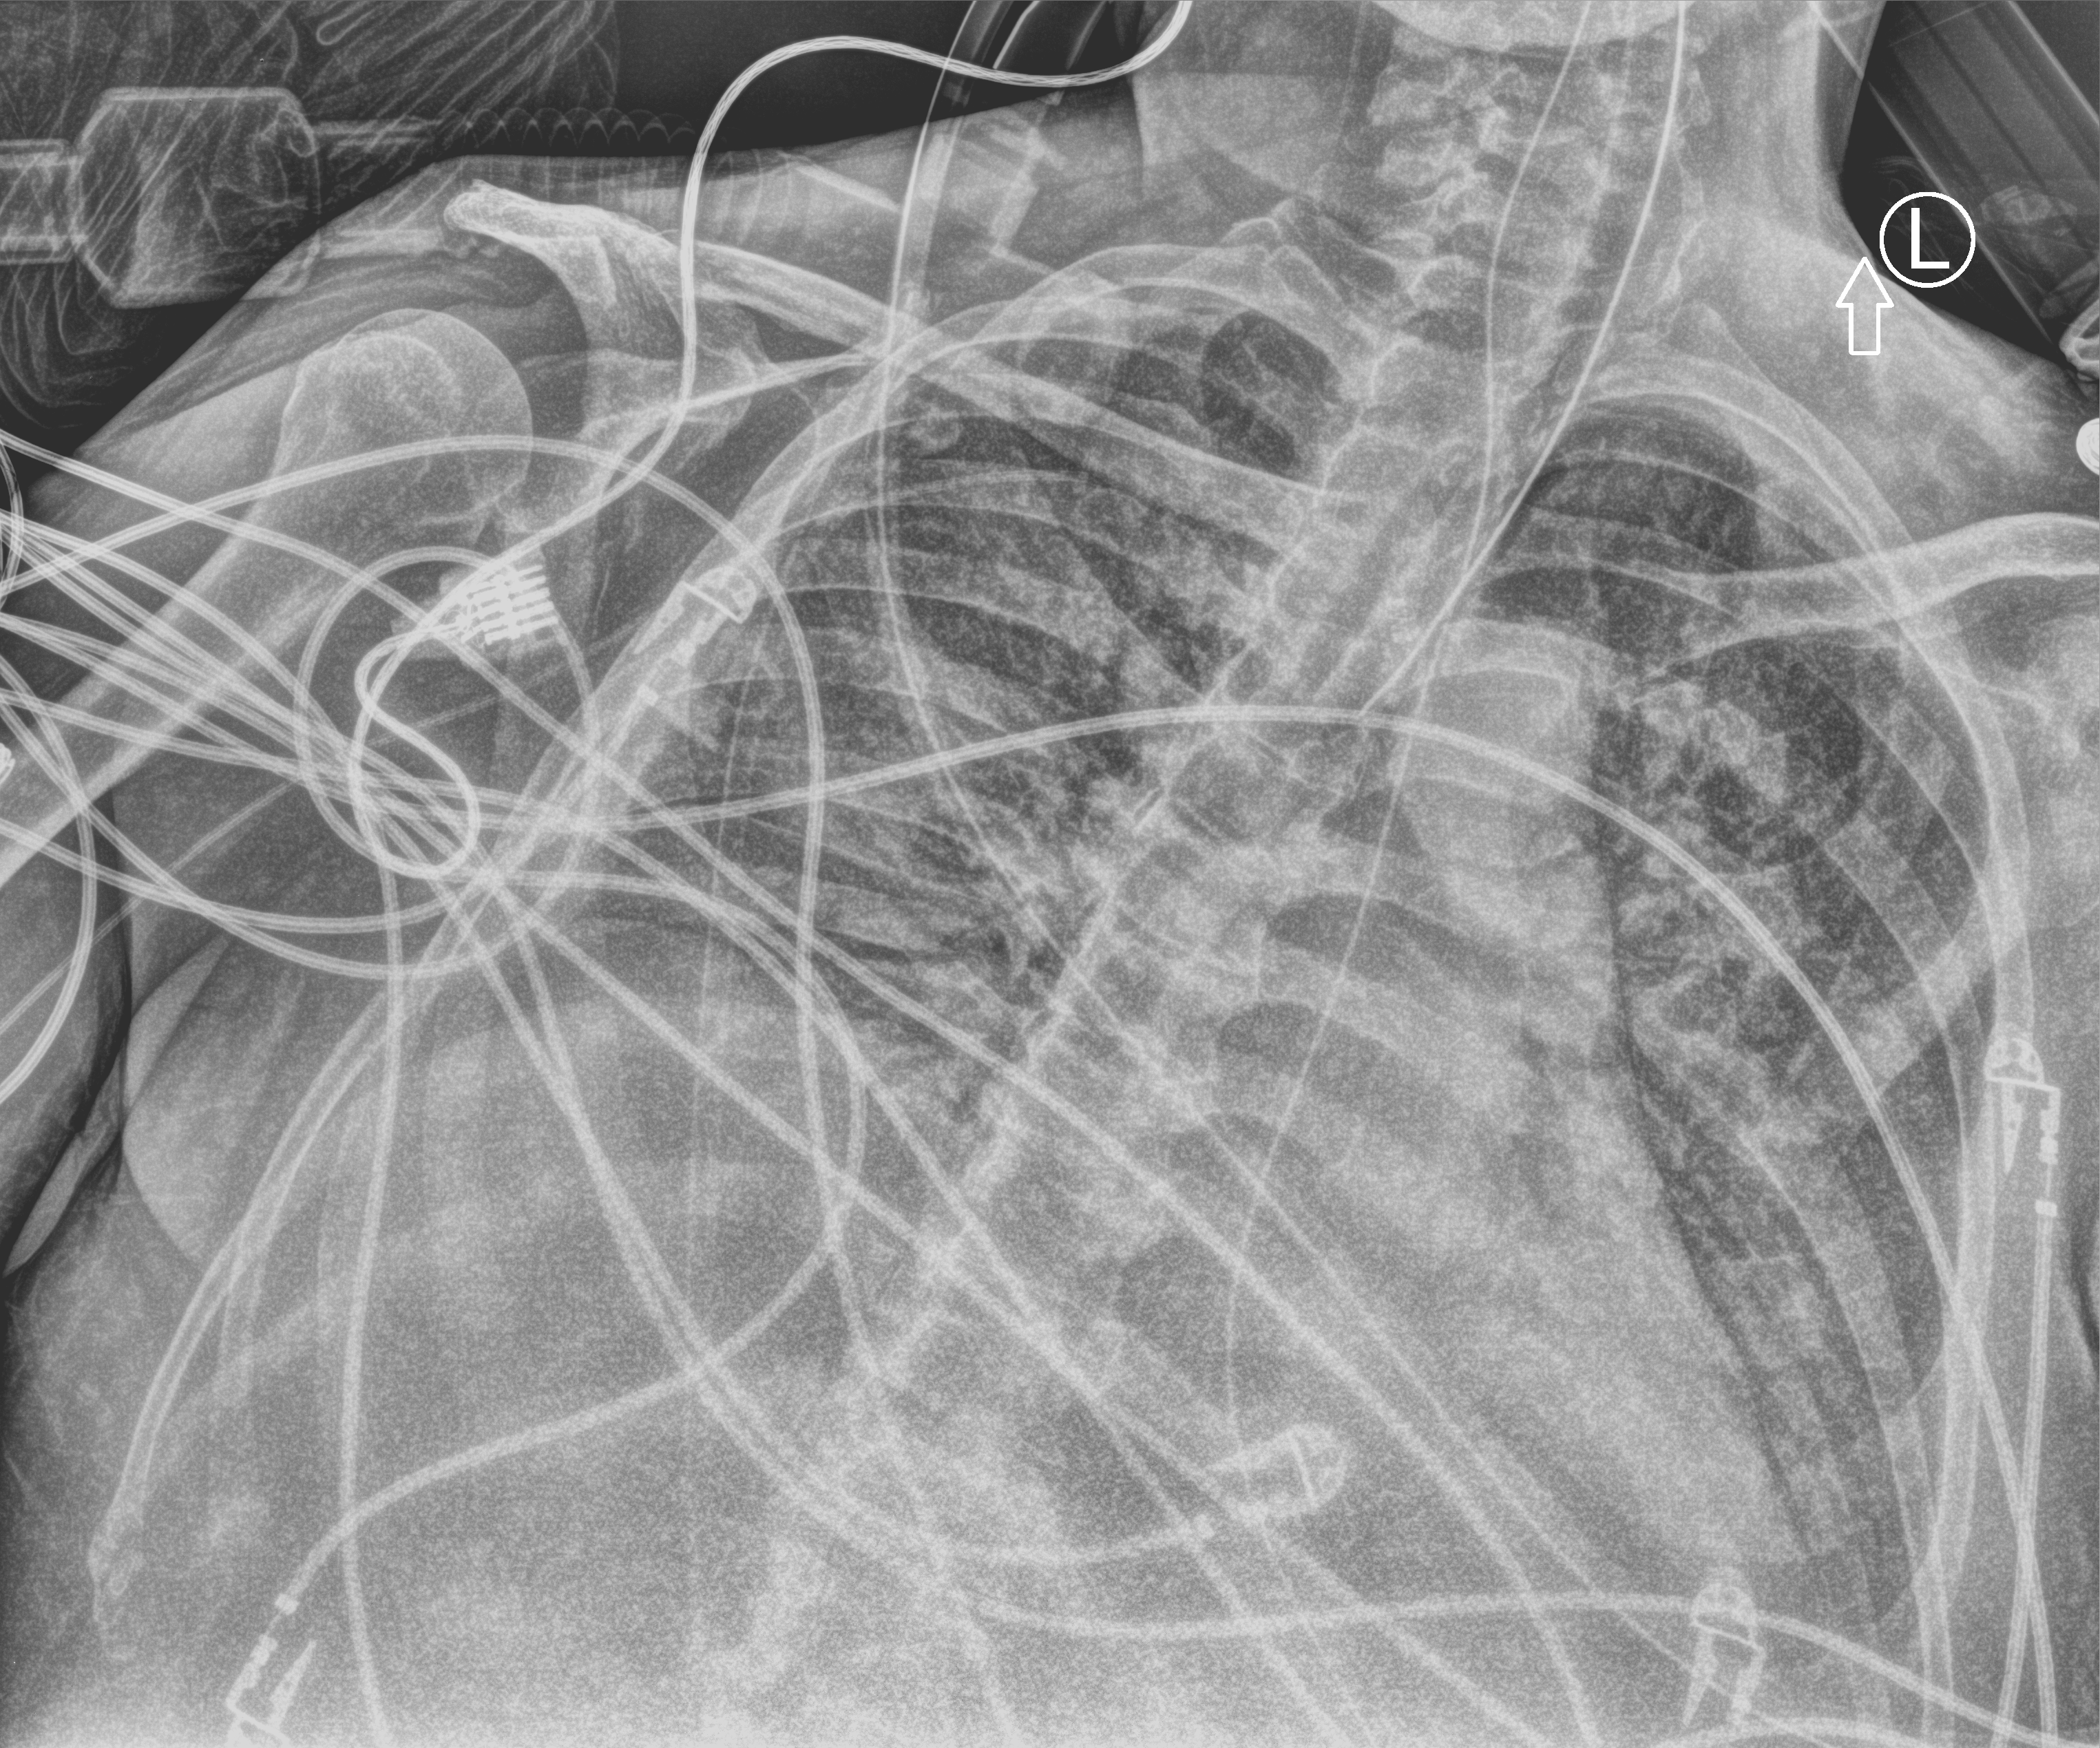
Chest X-ray (portable), anteroposterior (AP) projection. Male patient hospitalised with COVID-19, age 60–74 years.
From the hospital-stay record, not from the radiograph (when in the stay this image was taken is not recorded):
- chronic kidney disease (admission record): no
- admitted to intensive care during this hospital stay: yes